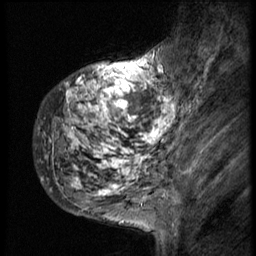
Breast MRI (dynamic contrast-enhanced), one sagittal slice; position 13 of 58 along the scan axis; 3 images stored at this slice position (order not interpretable as contrast timing); 1.5 T; TE 4.2 ms, TR 9 ms; 2.5 mm slice thickness; 256 × 256 image matrix, field of view 180 × 180 mm. Patient: female, 50 years. From the clinical record (not read from this slice): setting: breast cancer imaged before/during neoadjuvant chemotherapy; receptor status: triple-negative.
Outlined on this slice (semi-automatically segmented with operator editing):
- analysis volume of interest (the breast-tissue region the enhancement analysis was run in; not a lesion): bounding box [x1, y1, x2, y2] px = [35, 48, 186, 214]
- tumour enhancement mask (voxels above the 140 % enhancement threshold inside the analysis volume of interest): [39, 56, 186, 211]